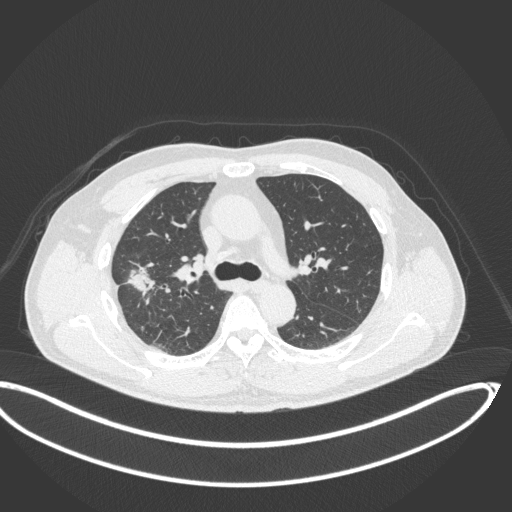
Chest CT, one axial slice. Slice 225 of 341 in the series (ordered by position). 120 kVp. Lung window (W 1500 / L -600 HU). 1 mm slice thickness. 512 × 512 image matrix. Male patient, age 63 years. Case-level facts recorded for this patient, not image findings: clinical TNM (as recorded): T1c N0 M0; histopathological grade: G2-3.
Structures marked on this image (bounding box drawn by a radiologist):
- lung tumour (recorded histology: adenocarcinoma): bounding box [x1, y1, x2, y2] px = [123, 255, 159, 303]